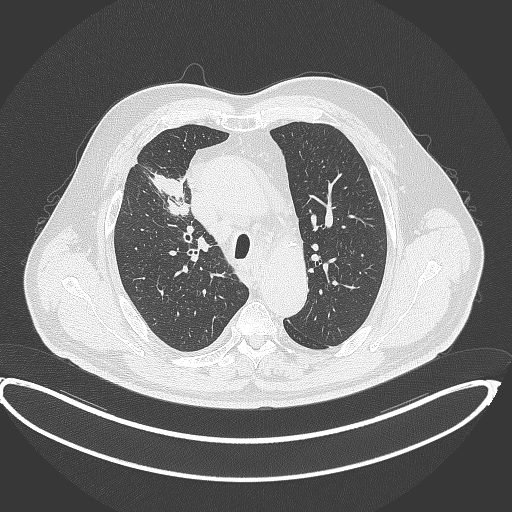
Chest CT, one axial slice. Position 292 of 390 along the scan axis. Reconstruction kernel B70f. 120 kVp. Lung window (W 1500 / L -600 HU). 512 × 512 image matrix. Male patient, age 62 years. Case-level facts recorded for this patient, not image findings: clinical TNM (as recorded): T1c N3 M1c.
Annotated regions visible in this slice (bounding box drawn by a radiologist):
- lung tumour (recorded histology: adenocarcinoma): bounding box <148,168,193,217> (left, top, right, bottom; pixels)